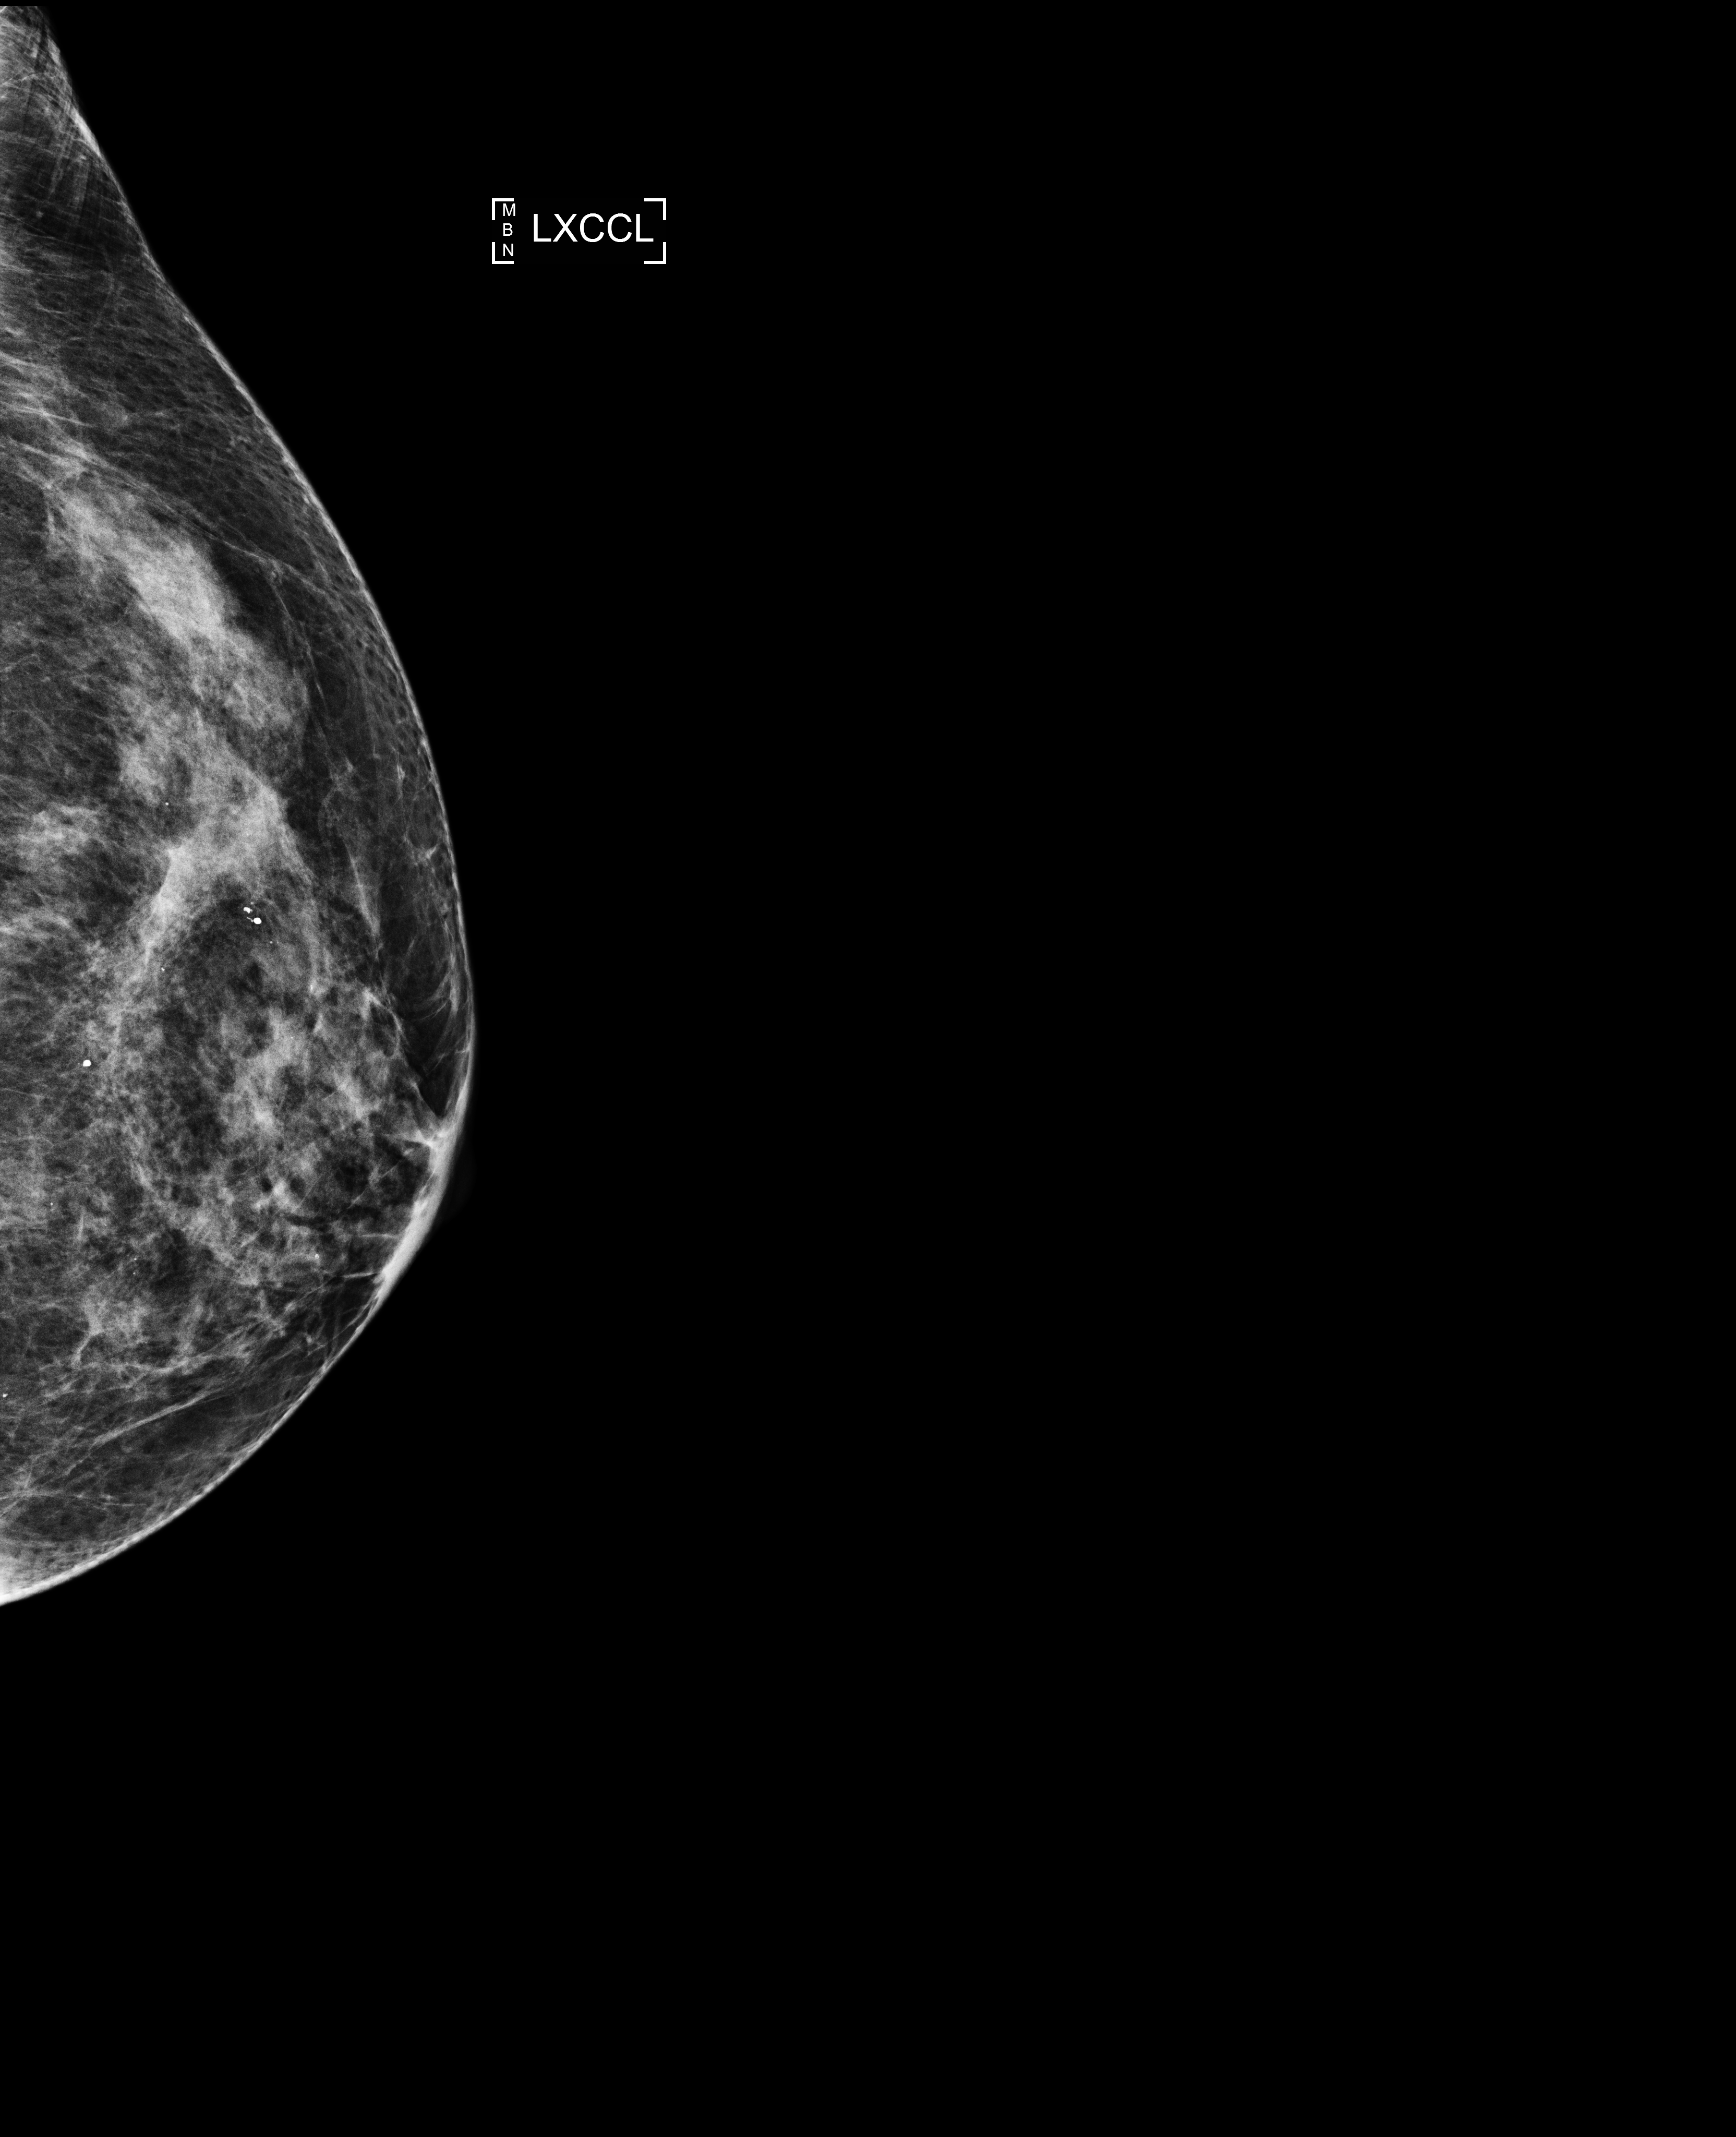
Screening examination. Patient: female, 75 years.
Image type: full-field digital mammogram. Breast: left. Projection: exaggerated CC view (lateral).